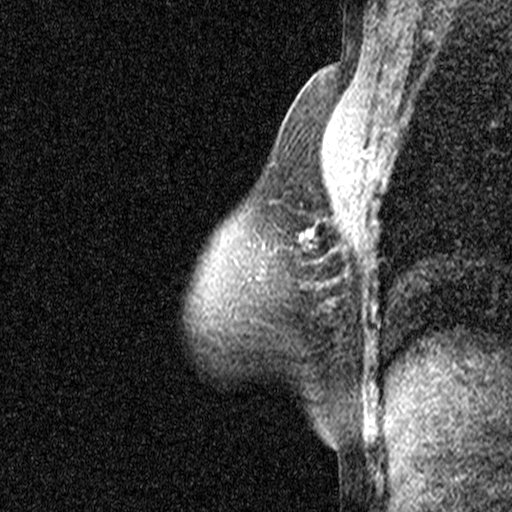
Breast MRI (dynamic contrast-enhanced), one sagittal slice. Position 33 of 44 along the scan axis. Dynamic contrast-enhanced study with each time point stored as its own series, time point 2 of 3 at this slice position (early post-contrast, ordered by acquisition time). 1.5 T. TE 4.5 ms, TR 11 ms. 512 × 512 image matrix, field of view 200 × 200 mm. Patient: female, 54 years. From the clinical record (not read from this slice): setting: breast cancer imaged before/during neoadjuvant chemotherapy; receptor status: HR-positive, HER2-negative.
Structures marked on this image (semi-automatic segmentation, software-assisted and operator-edited):
- analysis volume of interest (the breast-tissue region the enhancement analysis was run in; not a lesion): box from (x=214, y=200) to (x=333, y=325) px
- tumour enhancement mask (voxels above the 90 % enhancement threshold inside the analysis volume of interest): (x=299, y=233)–(x=302, y=240)